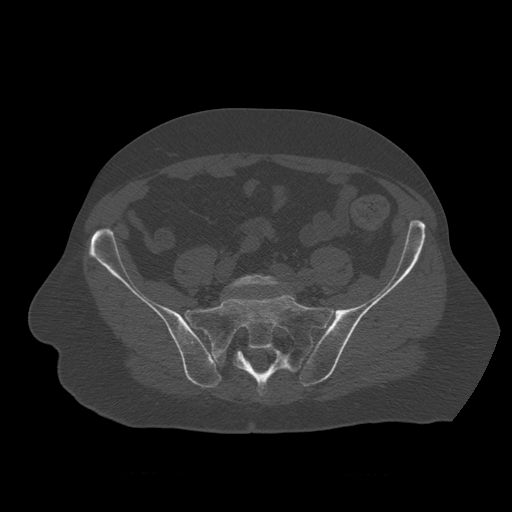
CT including the spine, one axial slice; slice 234 of 450 in the series (ordered by position); reconstruction kernel STANDARD; 120 kVp; bone window (W 1800 / L 400 HU); 1.25 mm slice thickness; 512 × 512 image matrix, field of view 405 × 405 mm. Patient age 75 years. Case-level facts recorded for this patient, not image findings: primary cancer: prostate.
Structures marked on this image (semi-automatic segmentation, software-assisted and operator-edited):
- L5 vertebra: bounding box (x1, y1, x2, y2) in pixels: (226, 275, 293, 293)